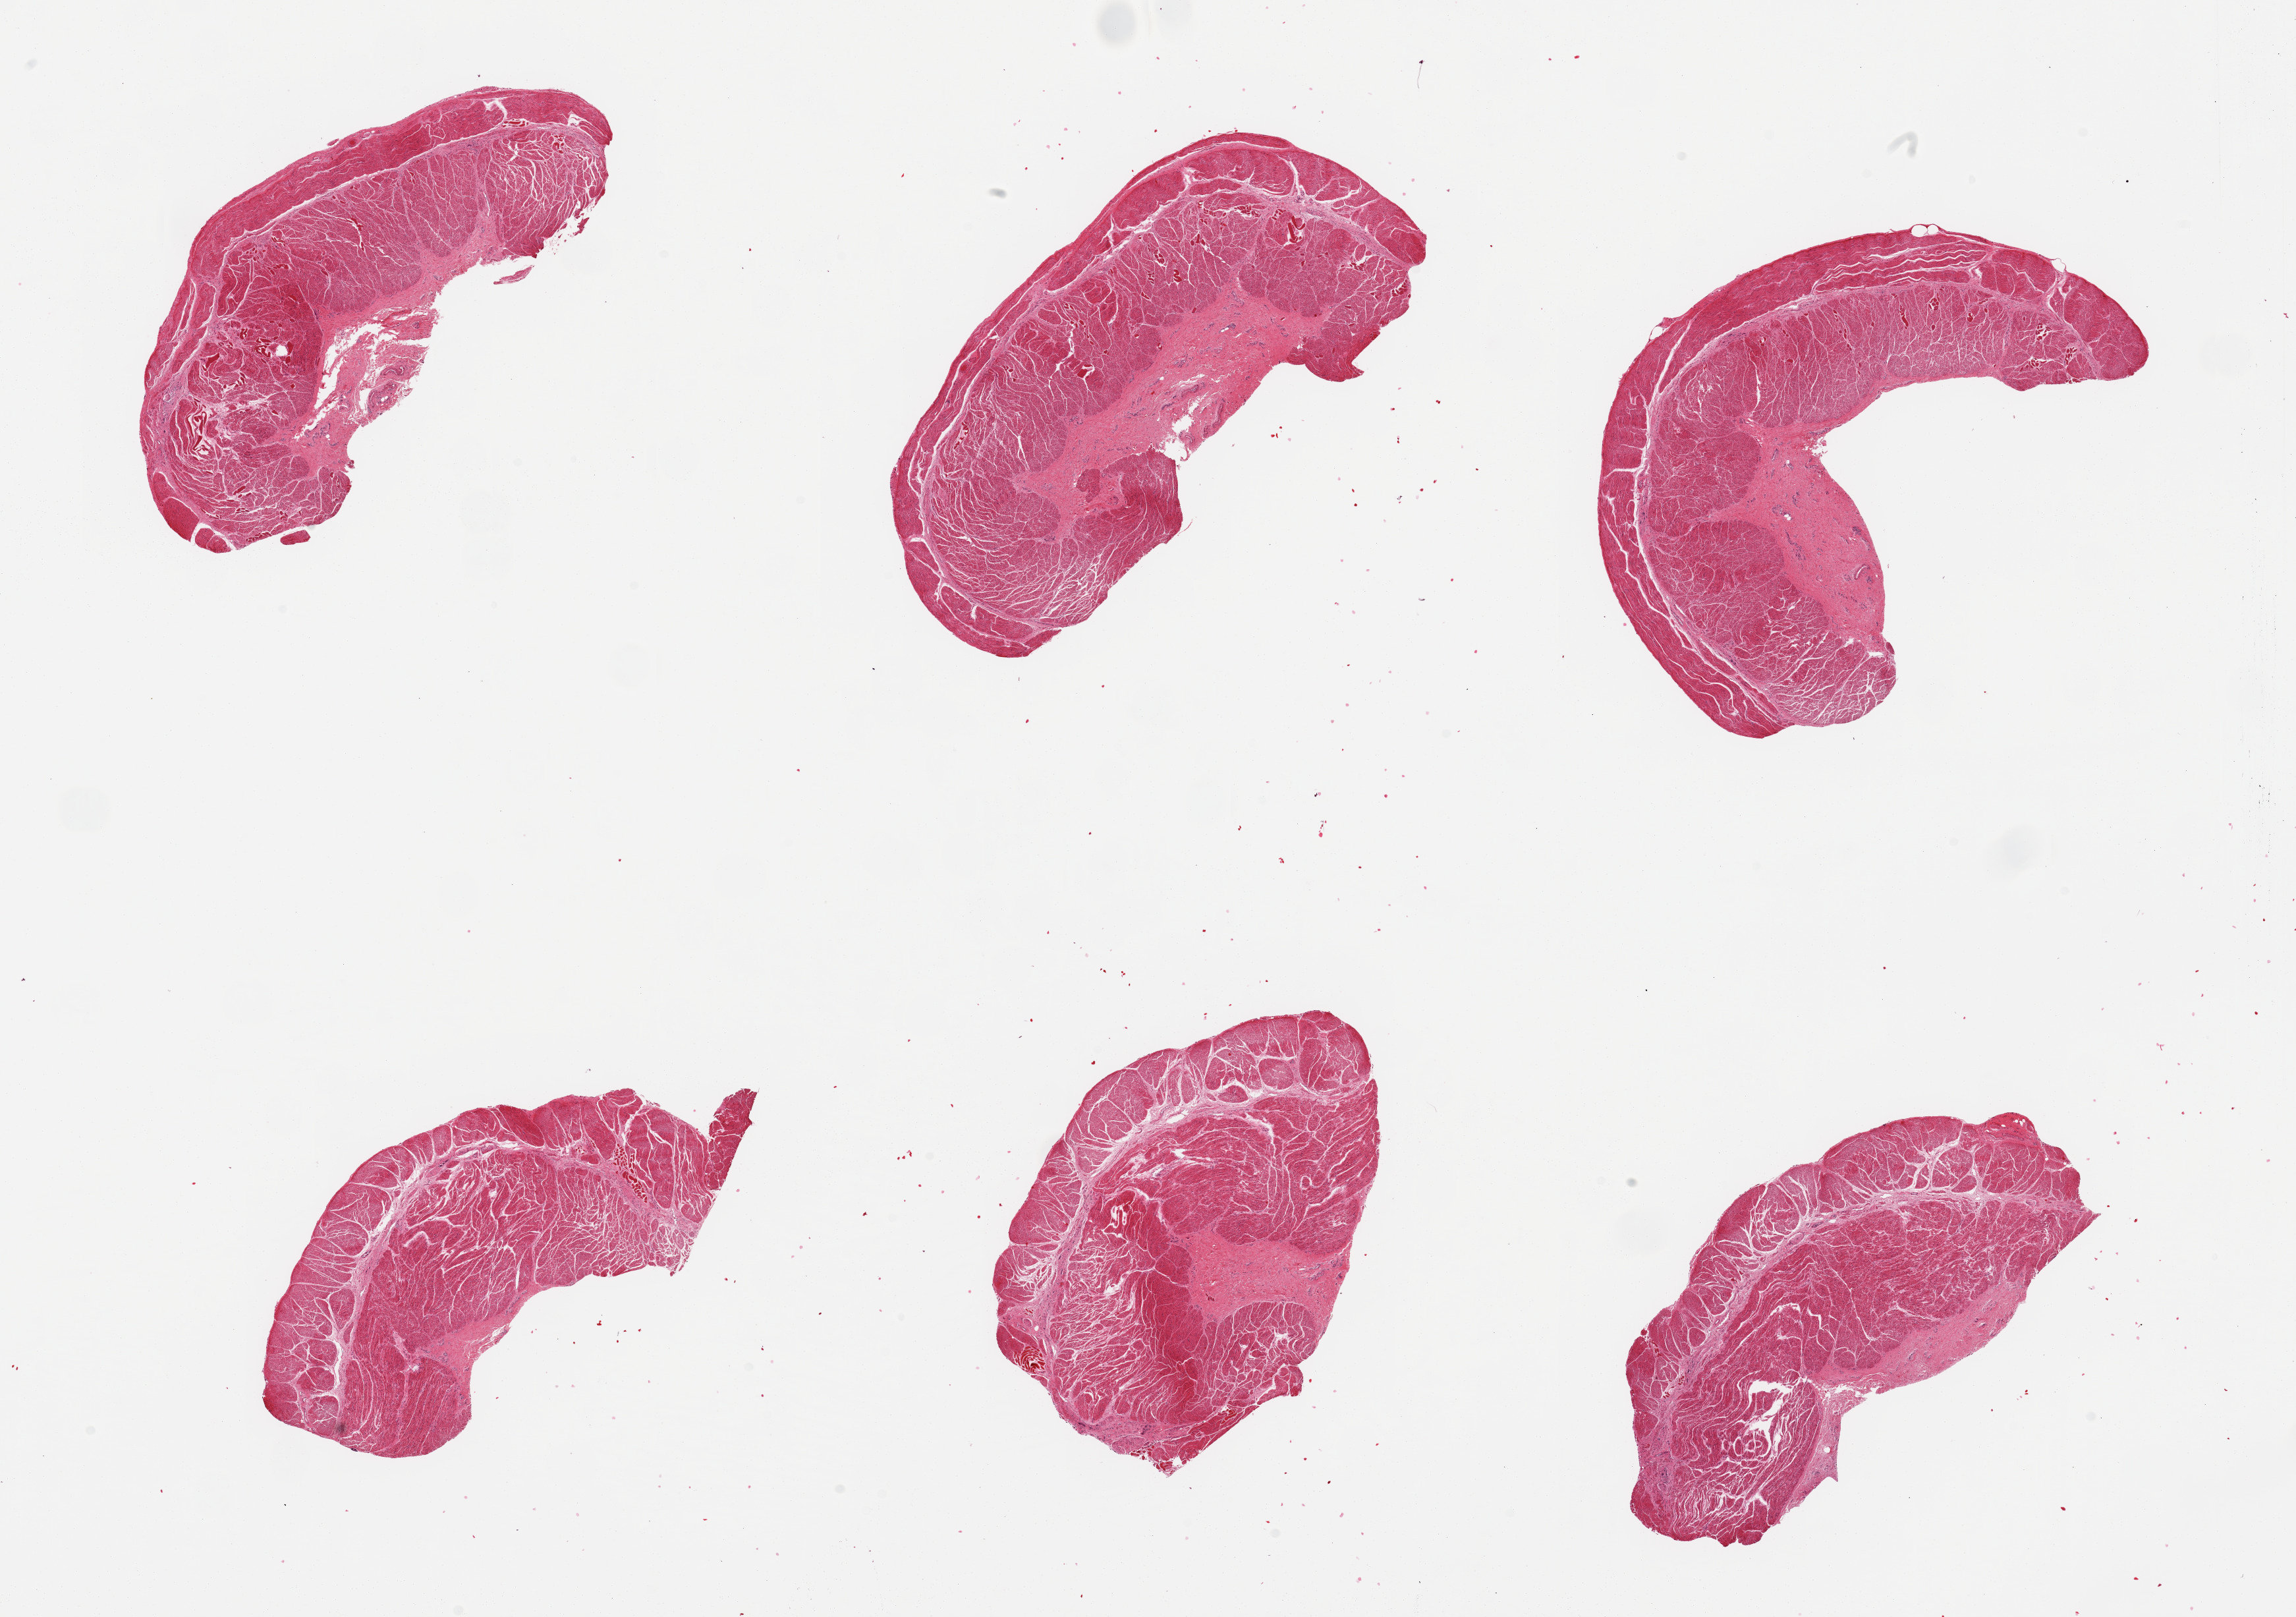
Haematoxylin and eosin whole-slide image — shown as a low-resolution overview of the whole scanned area (about 27.6 x 19.4 mm, acquisition: 20x scan). PAXgene-fixed paraffin-embedded (PFPE) section. Sampled site (target tissue): esophageal muscle. Tissue donor sample. Female donor.
Reviewer comment on this tissue sample: 6 pieces, well trimmed, admixture of smooth and skeletal muscle (skeletal muscle component is <10%).